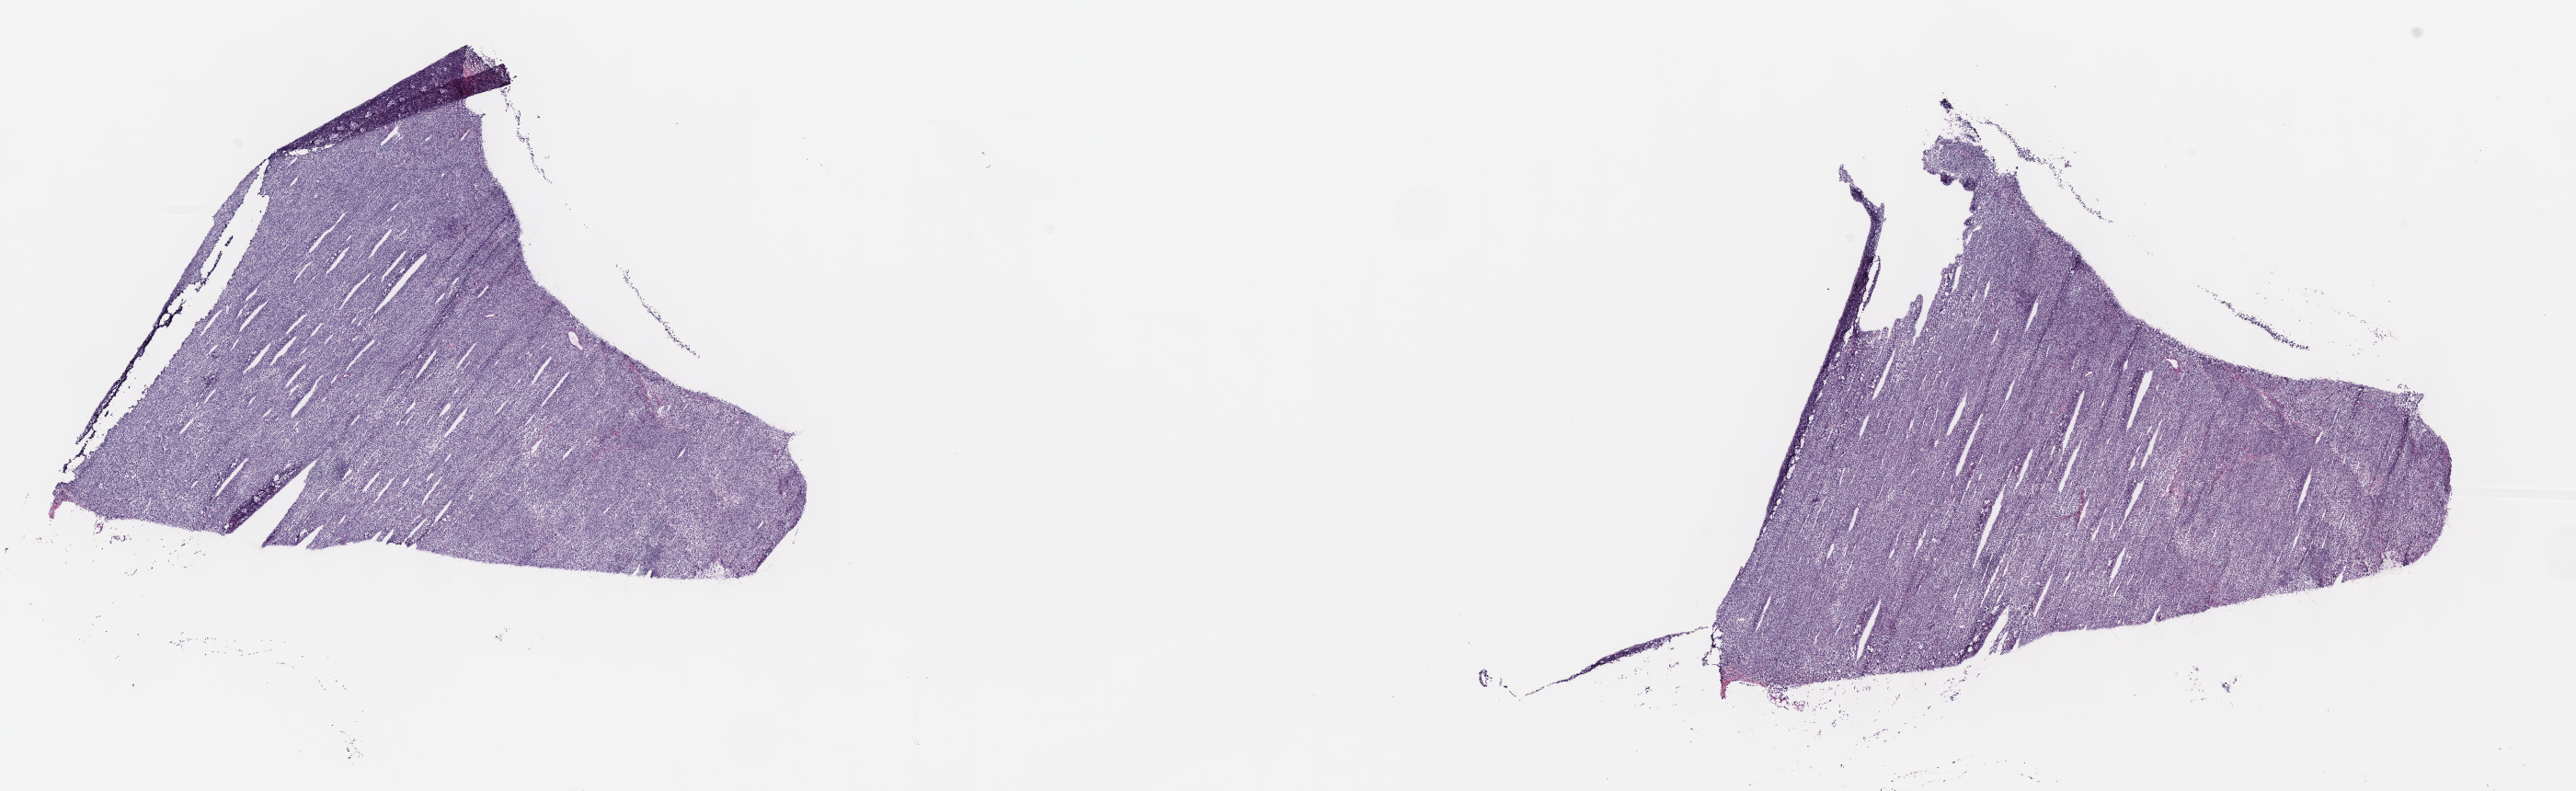
H&E-stained whole-slide image — whole scanned area (about 22.7 x 7.0 mm) shown as a low-resolution overview; frozen section from the top of the tissue portion; primary tumour sample from the lymphoid tissue. Male, age 72 years at initial diagnosis. Composition of this section per pathologist review: tumour cells 90%, tumour nuclei 90%, normal cells 5%, stromal cells 5%, necrosis 0%. Infiltration values recorded for this section: lymphocyte infiltration 80%, monocyte infiltration 10%, neutrophil infiltration 5%.
Histologic diagnosis: Diffuse large B-cell lymphoma, NOS (lymph nodes of head, face and neck).